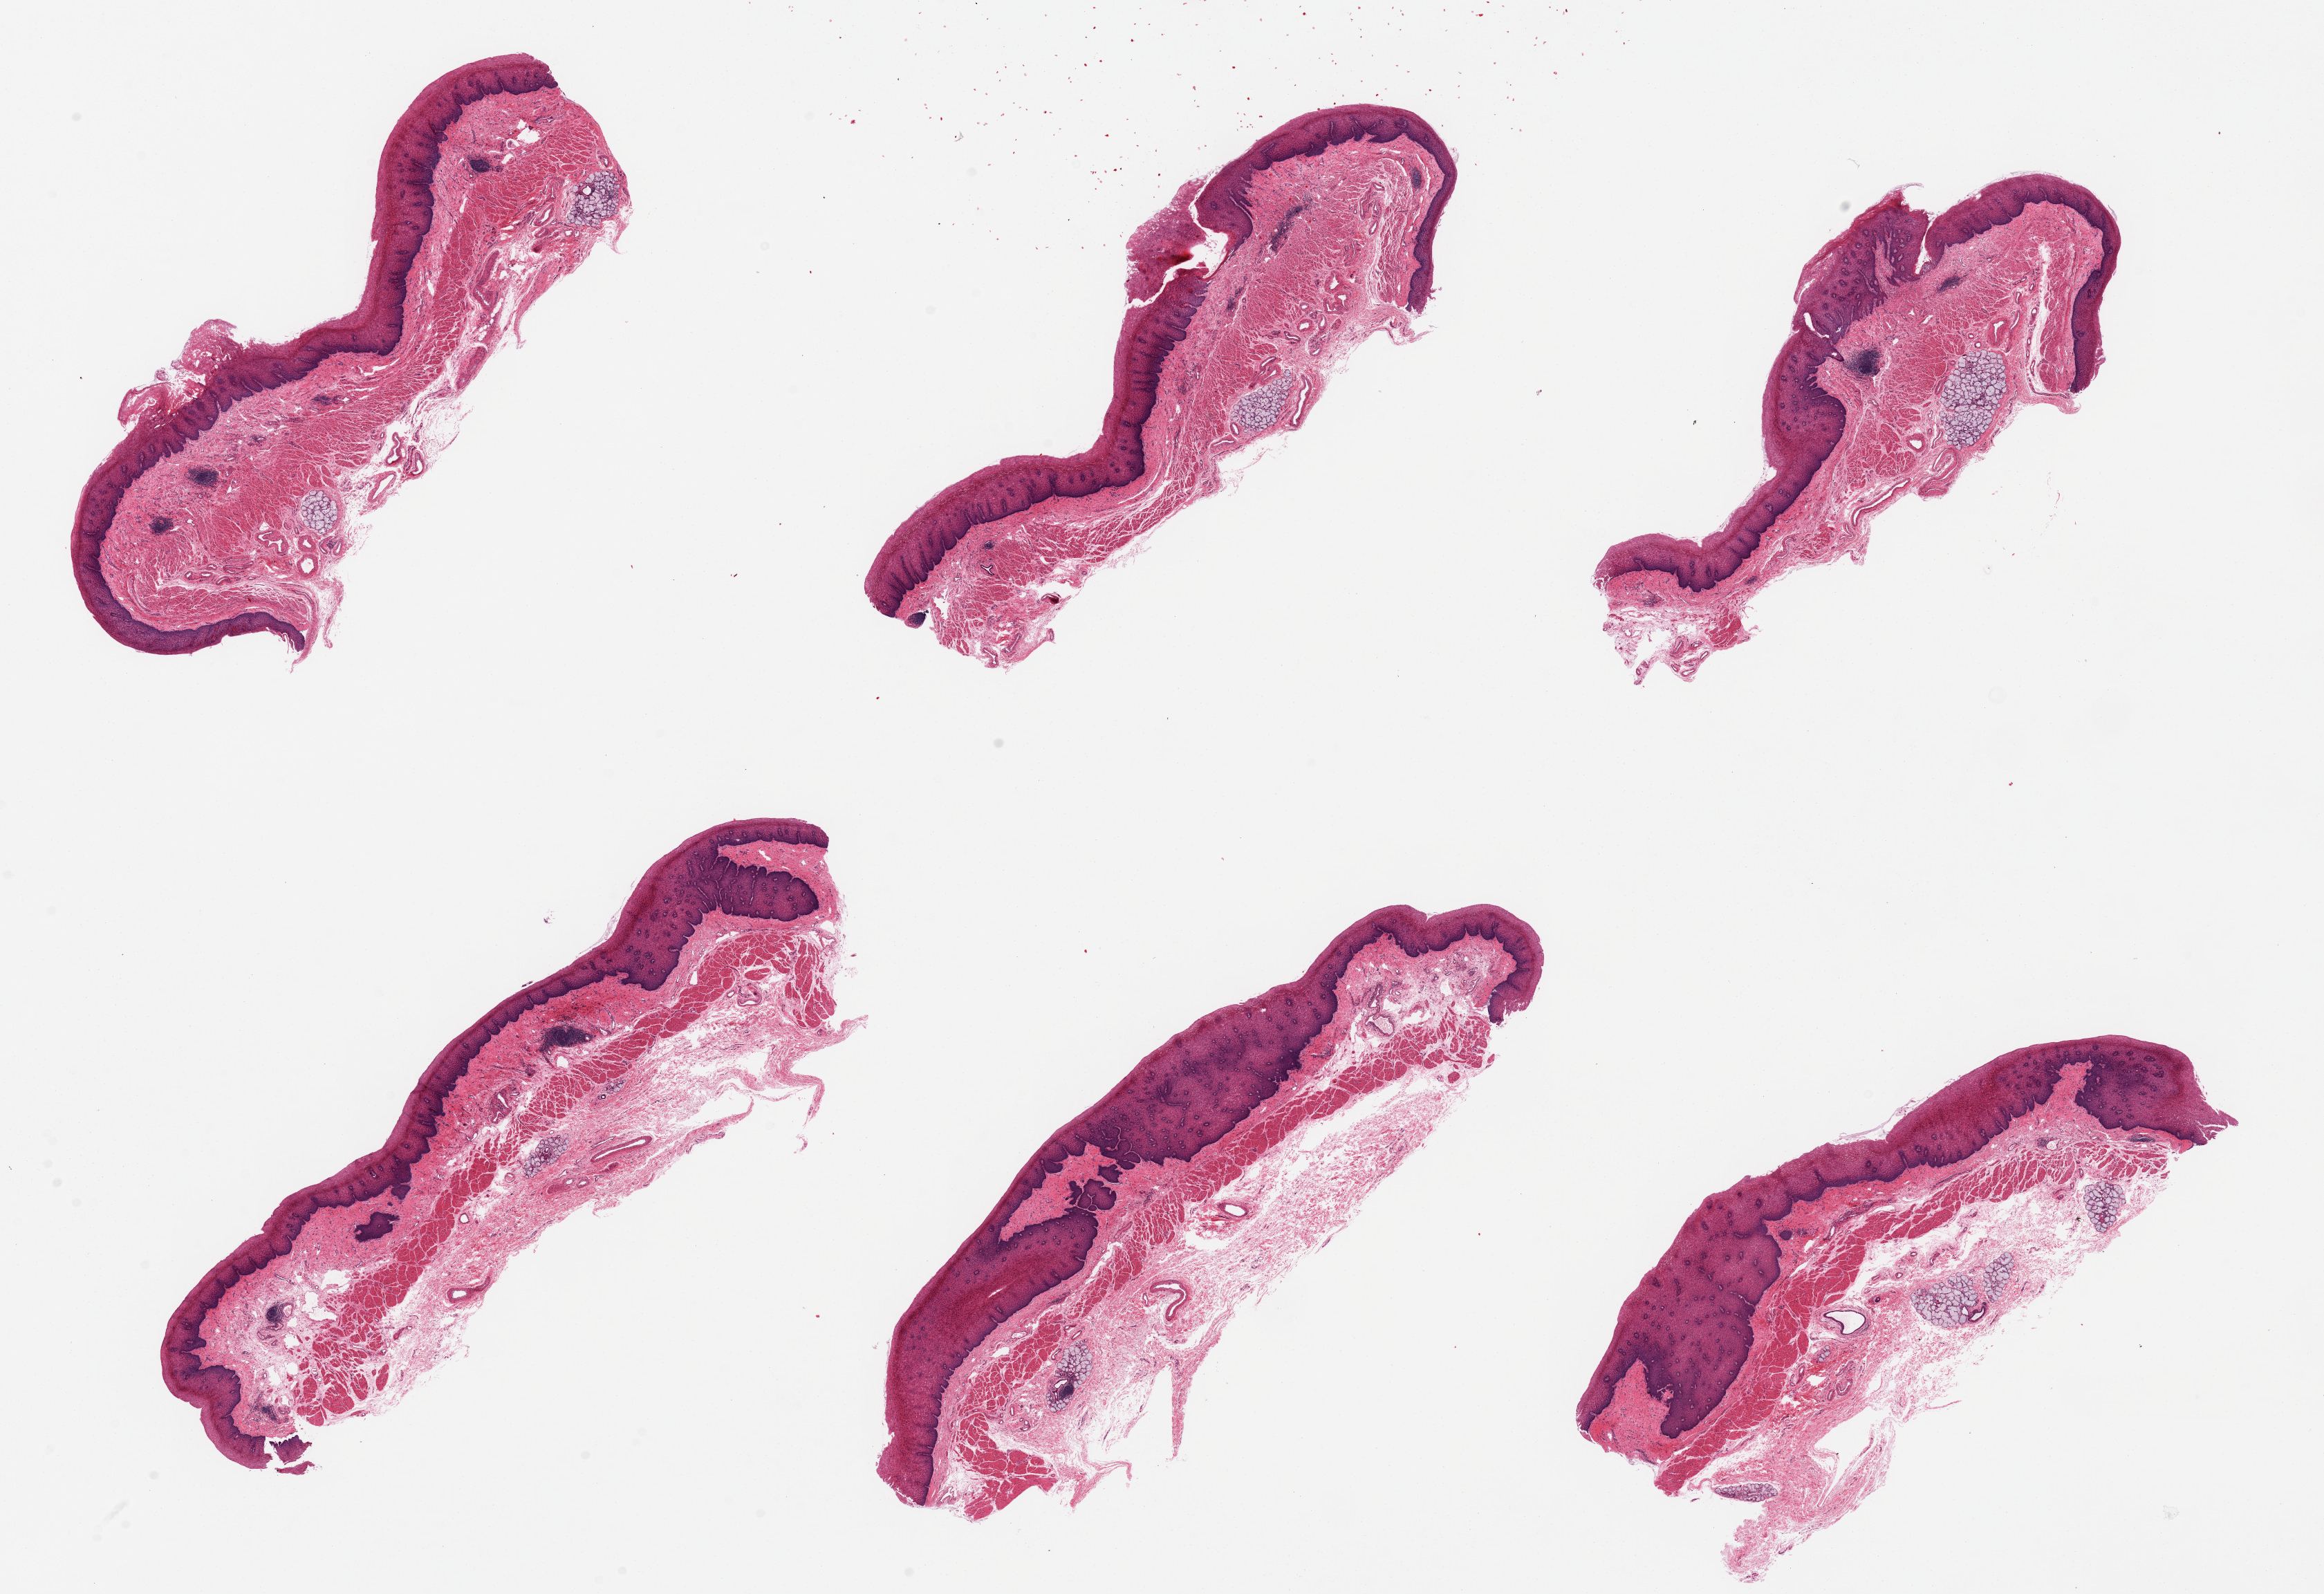
Whole-slide image, H&E stain — whole scanned area (about 26.6 x 18.2 mm) shown as a low-resolution overview; PAXgene-fixed paraffin-embedded (PFPE) section; target tissue: esophageal mucous membrane; tissue donor sample. Donor sex: male.
Review note (as recorded): 6 pieces, squamous mucosa is ~0.5mm thick, ~20% total; a few submucosal mucus glands noted.